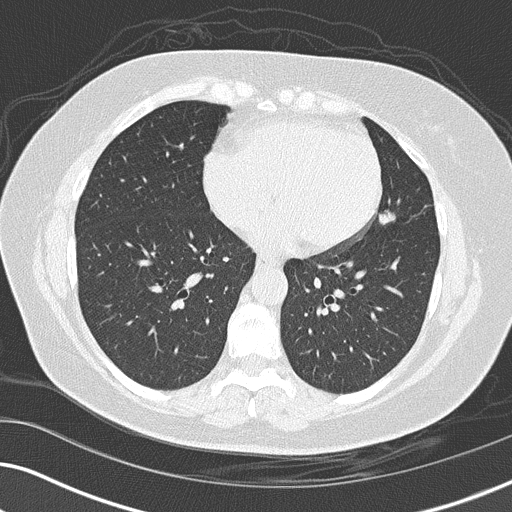
Low-dose screening chest CT, axial slice. Third screening round (two years after baseline). Lung window (W 1500 / L -600 HU). 2 mm slice thickness. Slice 88 of 152 in the series. Female participant, aged 56 years at enrolment.
Expert-annotated lung lesion, bounding box (x1, y1, x2, y2) in pixels: (358, 197, 410, 244). The exam's reader record, not a measurement of the box and not confirmed to be the same lesion: non-calcified nodule or mass ≥4 mm, lingula, 14 × 14 mm, spiculated (stellate) margins, soft tissue attenuation, pre-existing on the prior screen: yes; interval growth: yes. Official screen result: positive, other.